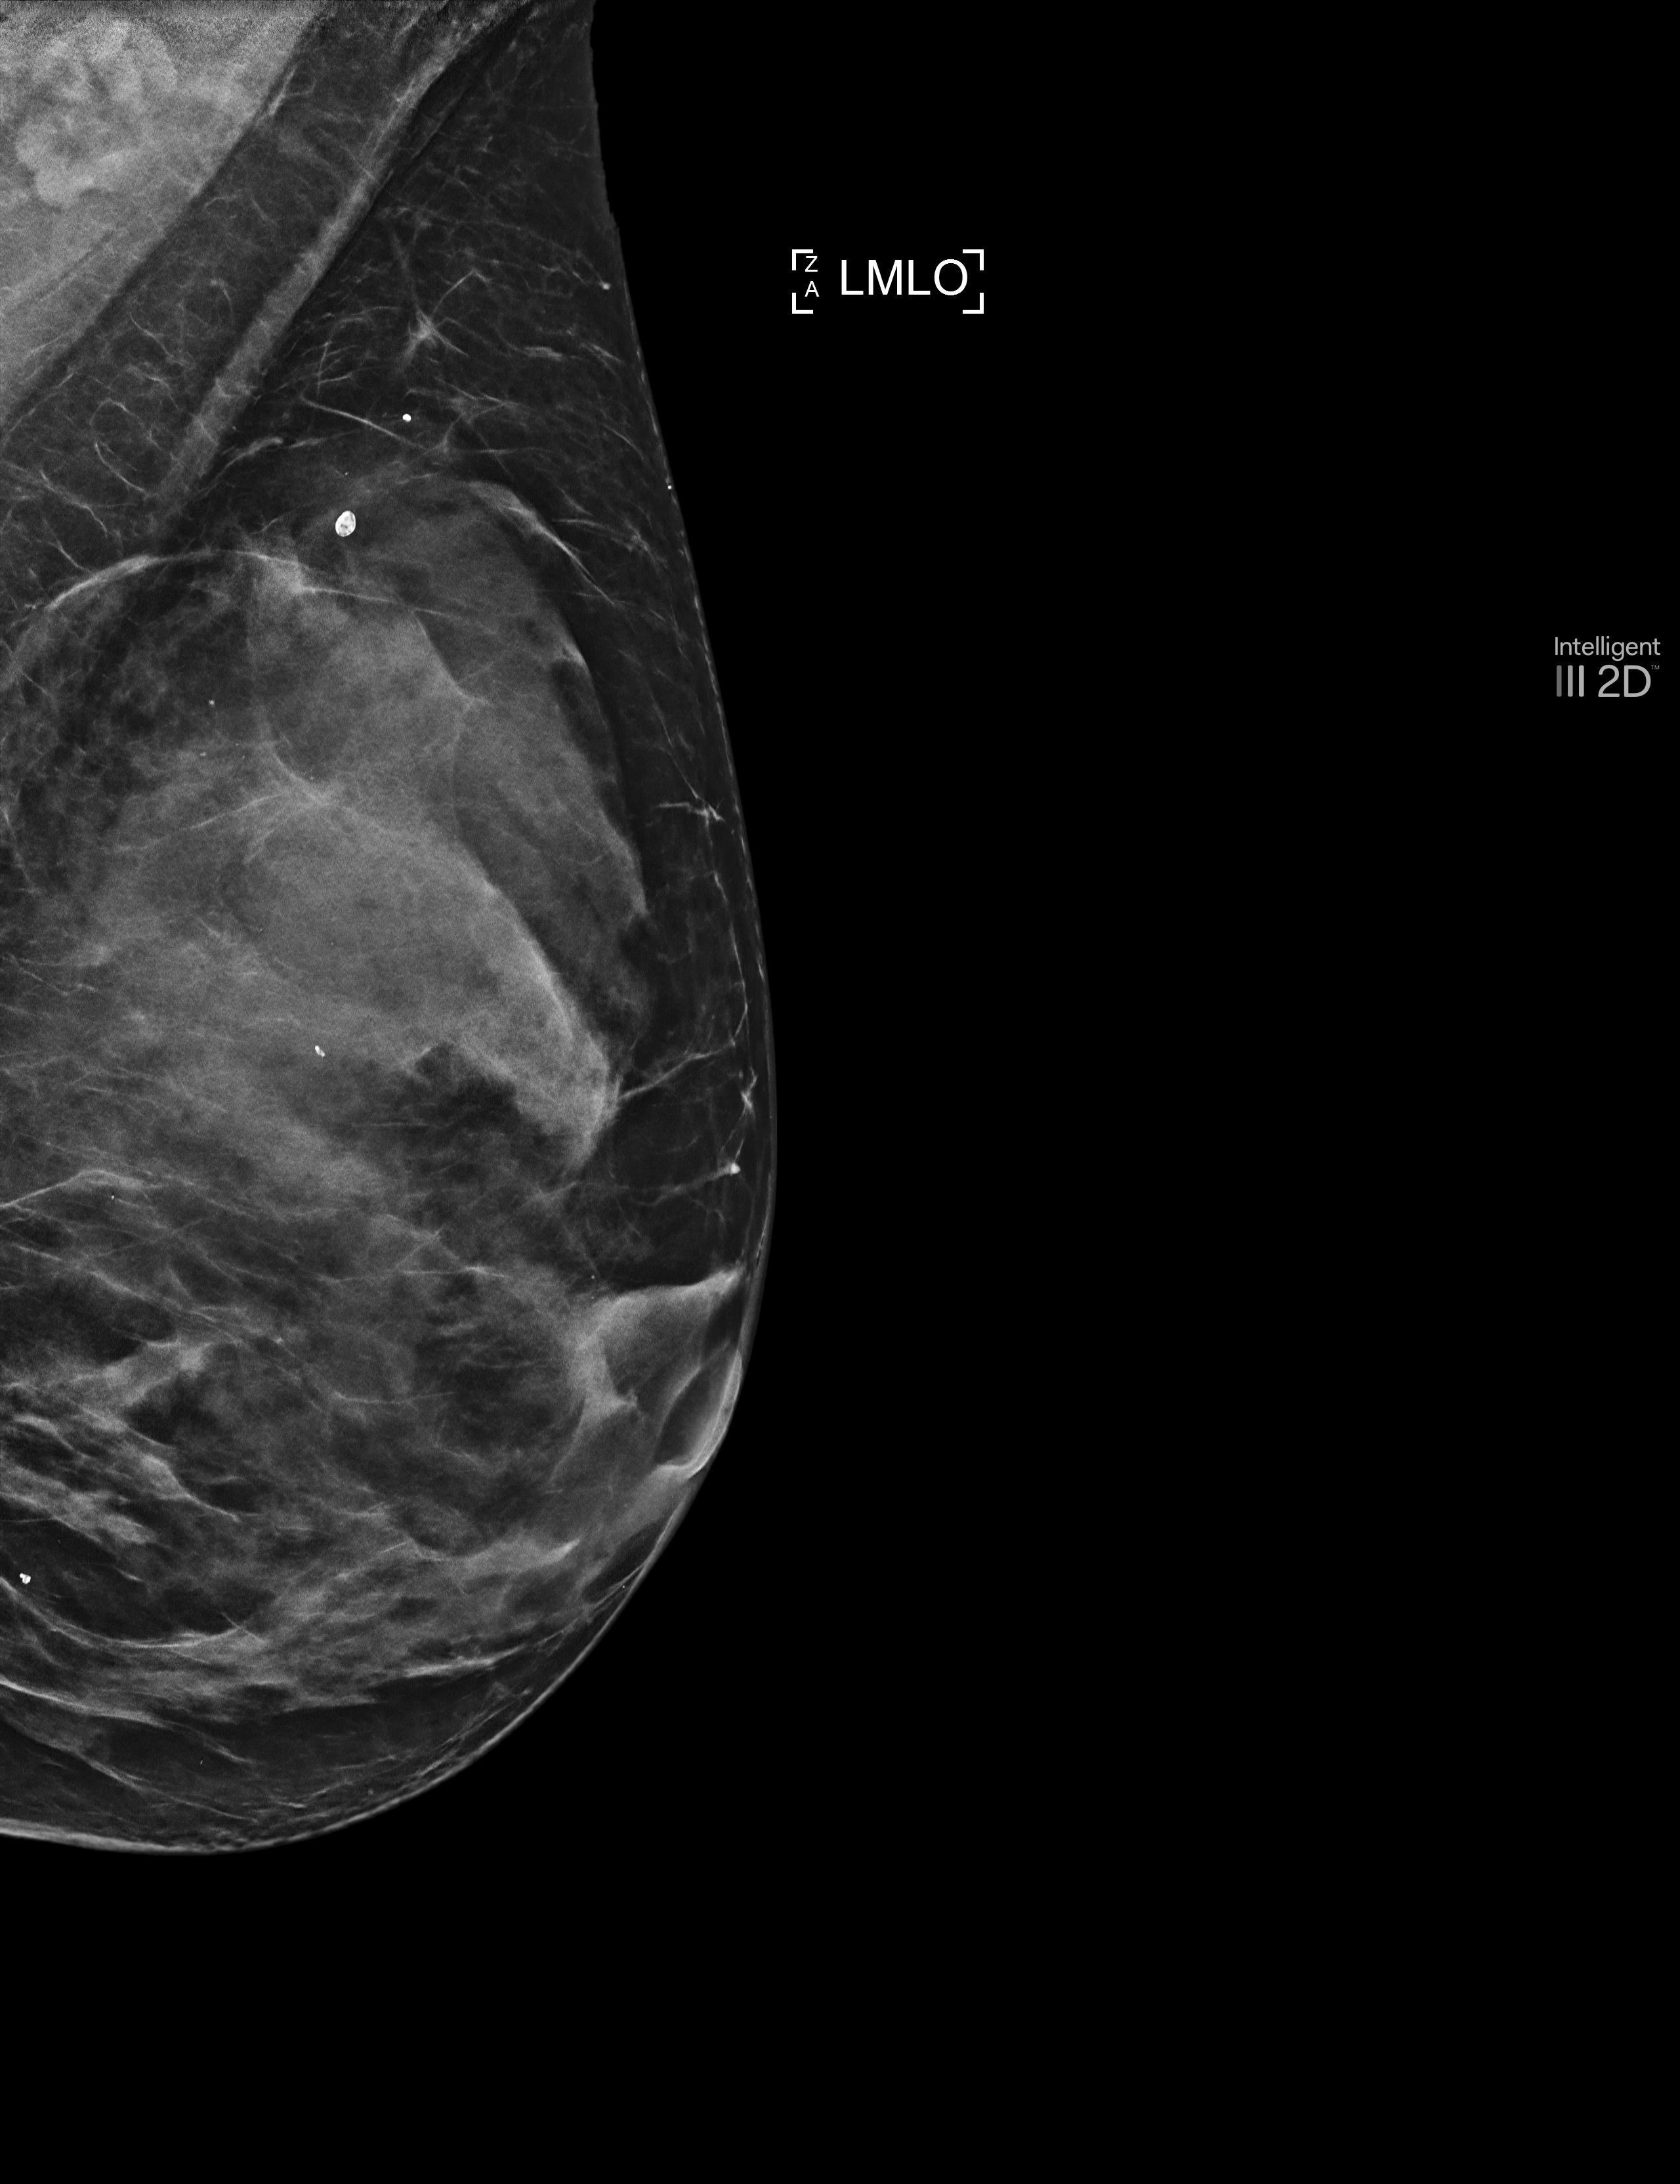
Screening examination, system: Selenia Dimensions.
Image type: synthesized 2-D view from tomosynthesis. Breast: left. Projection: MLO view.